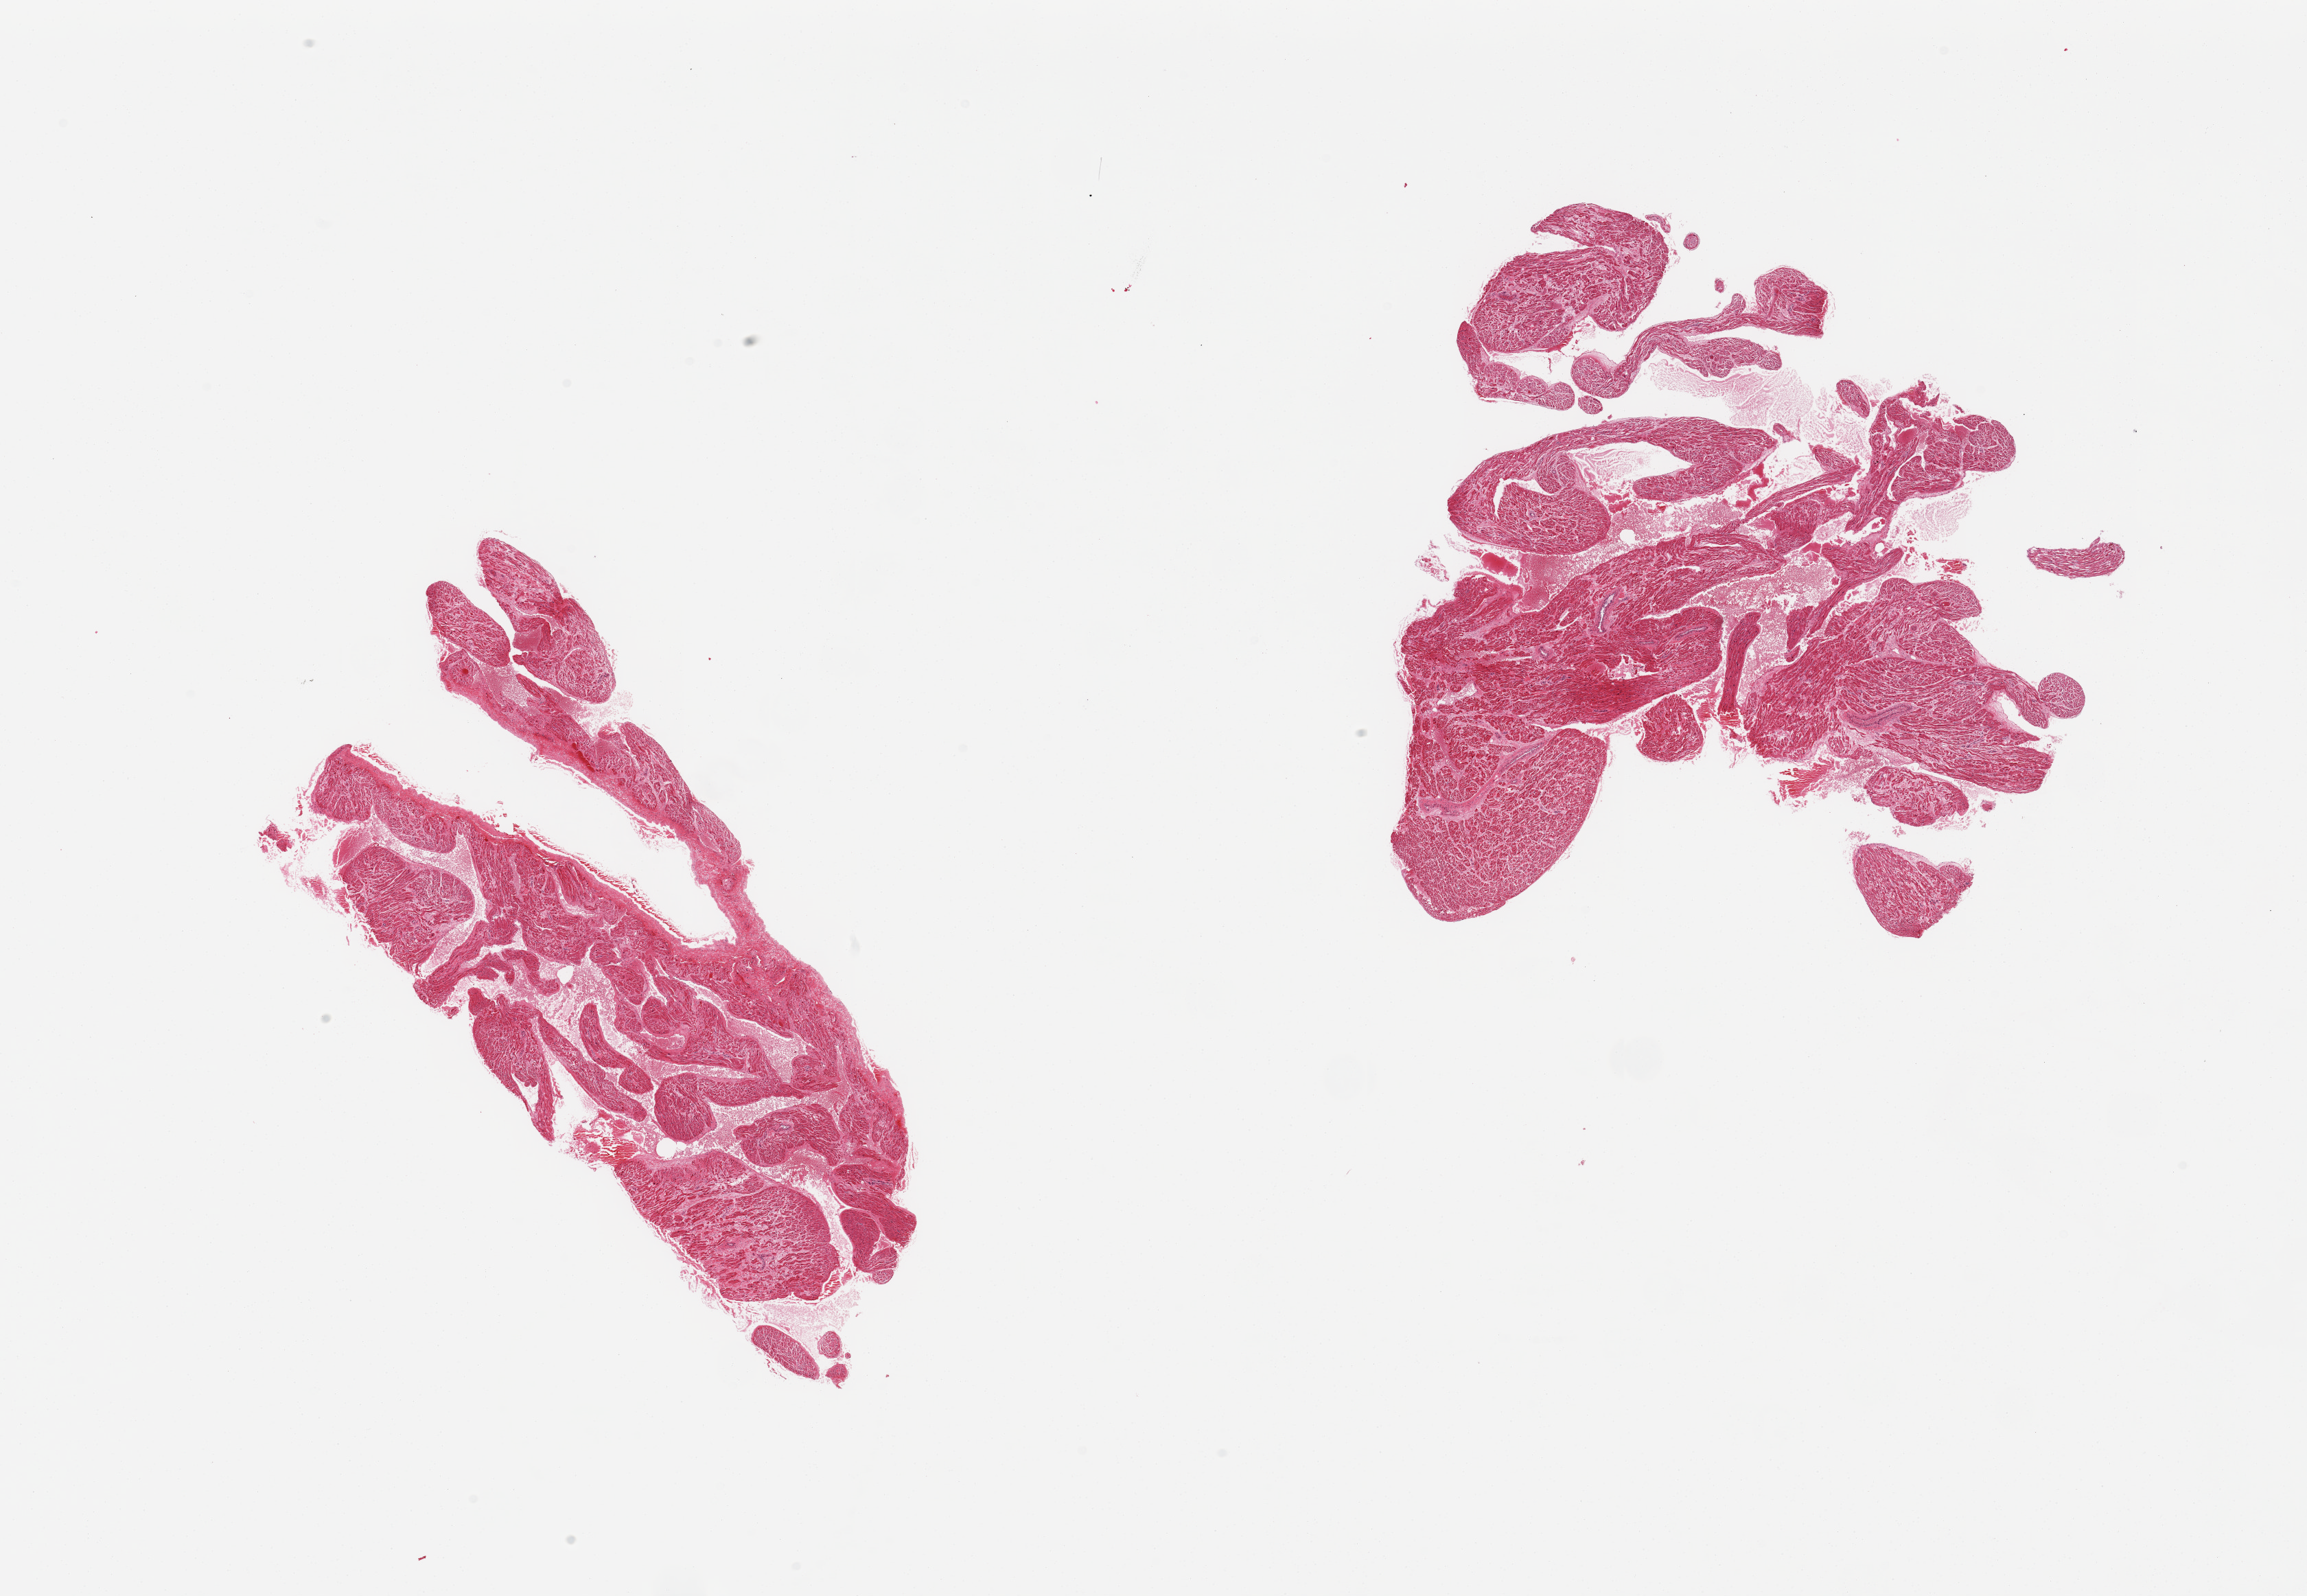
Digitized haematoxylin and eosin-stained section, whole scanned area (about 26.6 x 18.4 mm) shown as a low-resolution overview; PAXgene-fixed paraffin-embedded (PFPE) section; target tissue: auricular appendage; tissue donor sample.
Reviewer comment on this tissue sample: 2 pieces; no fat.